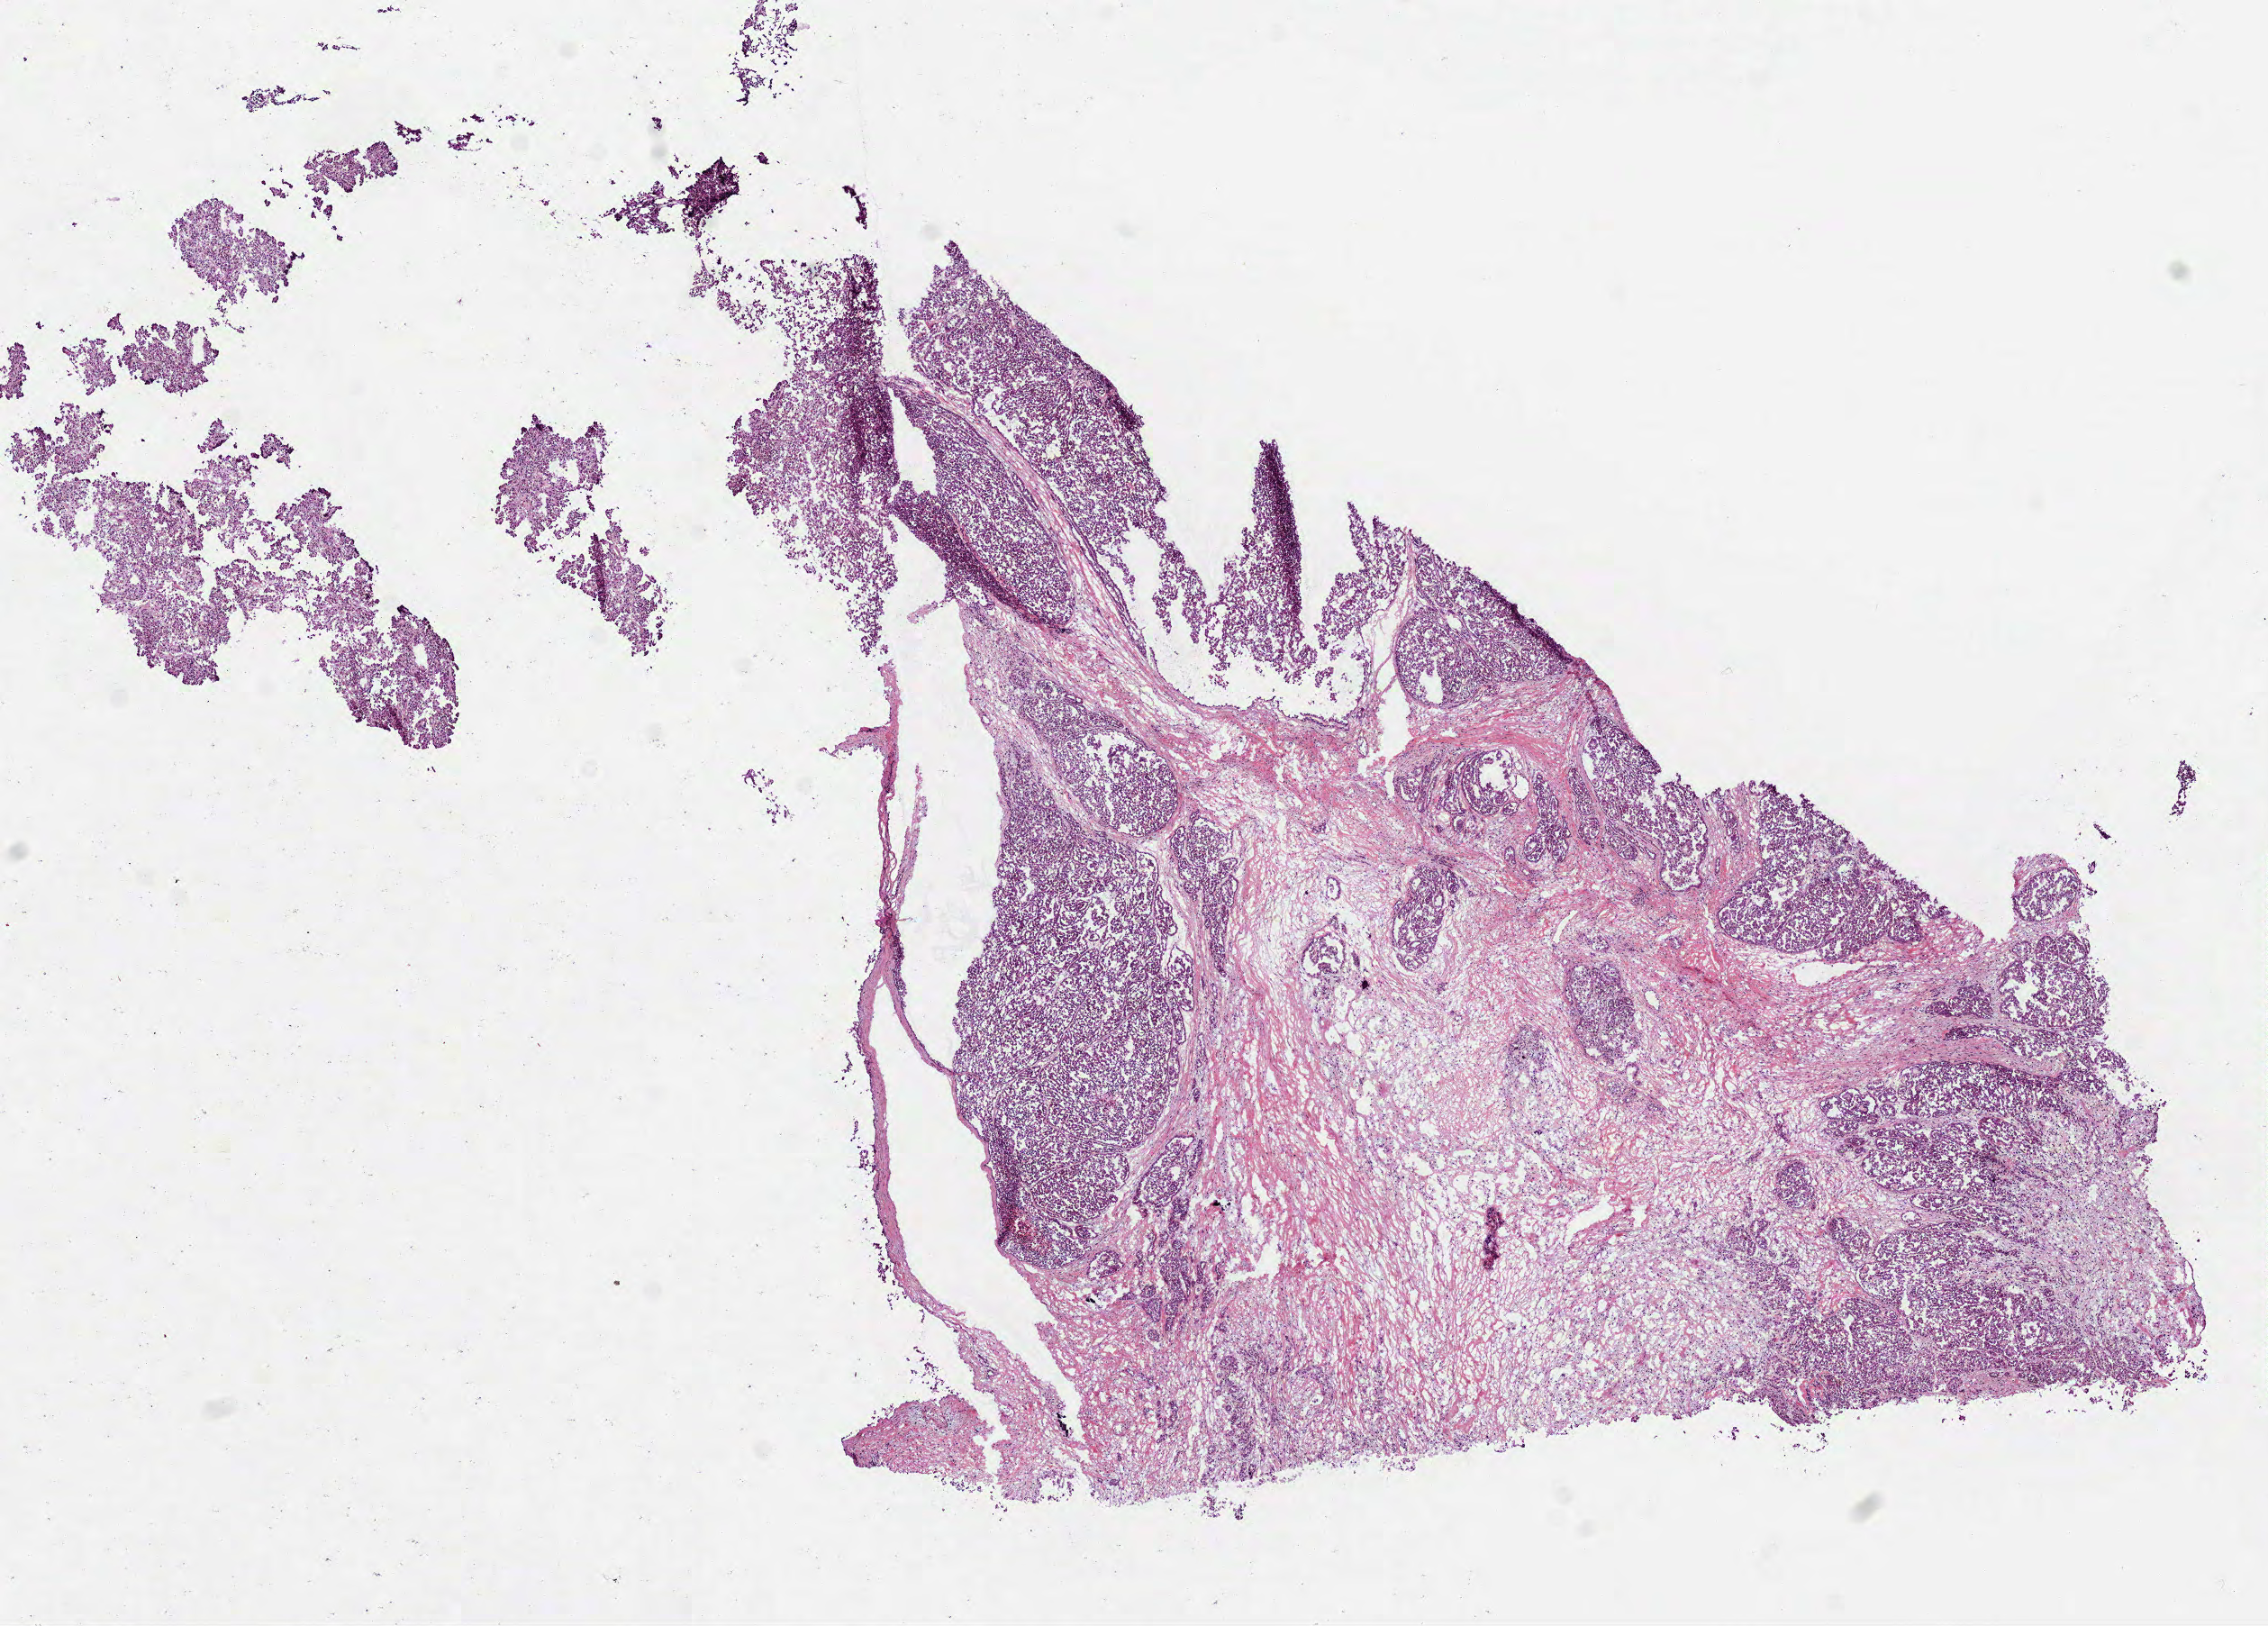
Whole-slide histology image, H&E, shown as a low-resolution overview of the whole scanned area (about 10.2 x 7.3 mm). Frozen section from the bottom of the tissue portion. Primary tumour sample from the kidney. Patient: female, age at initial diagnosis 75 years. Pathologist review of this section (percent, as recorded): tumour cells 70%, tumour nuclei 75%, normal cells 0%, stromal cells 30%, necrosis 0%. Infiltration values recorded for this section: lymphocyte infiltration 3%, monocyte infiltration 2%, neutrophil infiltration 0%.
Laterality: right. Pathologic diagnosis: Papillary adenocarcinoma, NOS. AJCC pathologic stage: III.